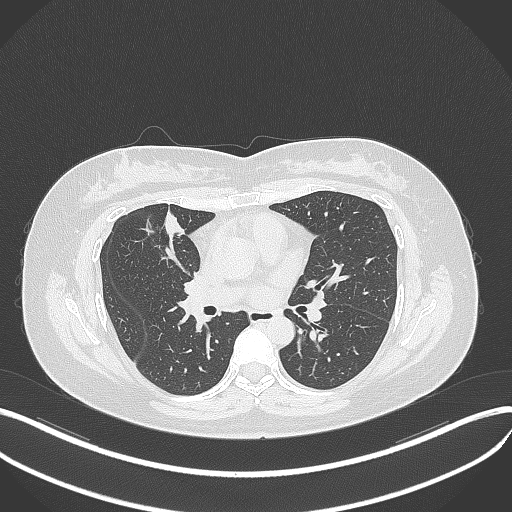
Chest CT, one axial slice; reconstruction kernel B70f; 120 kVp; lung window (W 1500 / L -600 HU); 1 mm slice thickness; 512 × 512 image matrix, field of view 400 × 400 mm. Female patient, age 42 years. Case-level facts recorded for this patient, not image findings: clinical TNM (as recorded): T1b N0 M0.
Outlined on this slice (rectangle marked by the reading radiologist):
- lung tumour (recorded histology: adenocarcinoma): bounding box <157,210,188,243> (left, top, right, bottom; pixels)